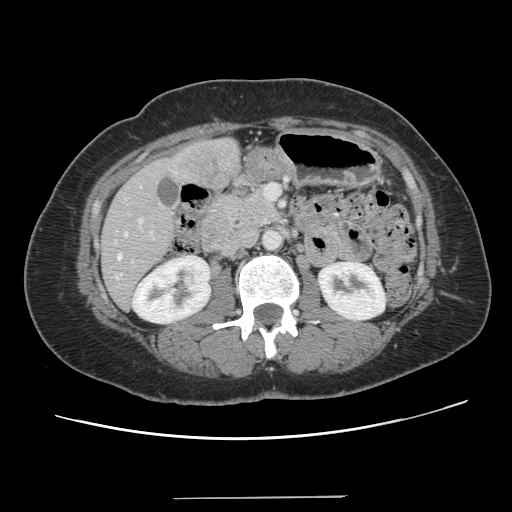
Contrast-enhanced abdominal CT, one axial slice. Slice 50 of 141 in the series (ordered by position). Intravenous contrast given. Soft-tissue window (W 400 / L 40 HU). 2.5 mm slice thickness. 512 × 512 image matrix, field of view 366 × 366 mm. Female patient, age 53 years. Case-level facts recorded for this patient, not image findings: diagnosis: colorectal cancer liver metastases, imaged before liver resection; multiple liver metastases: no; largest metastasis: 14.5 cm.
Annotated regions visible in this slice (outlined manually by an expert reader):
- hepatic veins: bounding box (x1, y1, x2, y2) in pixels: (117, 232, 127, 259)
- liver: (100, 139, 239, 308)
- planned liver remnant (the part of the liver to remain after resection): (100, 219, 175, 308)
- liver metastasis: (182, 148, 231, 184)